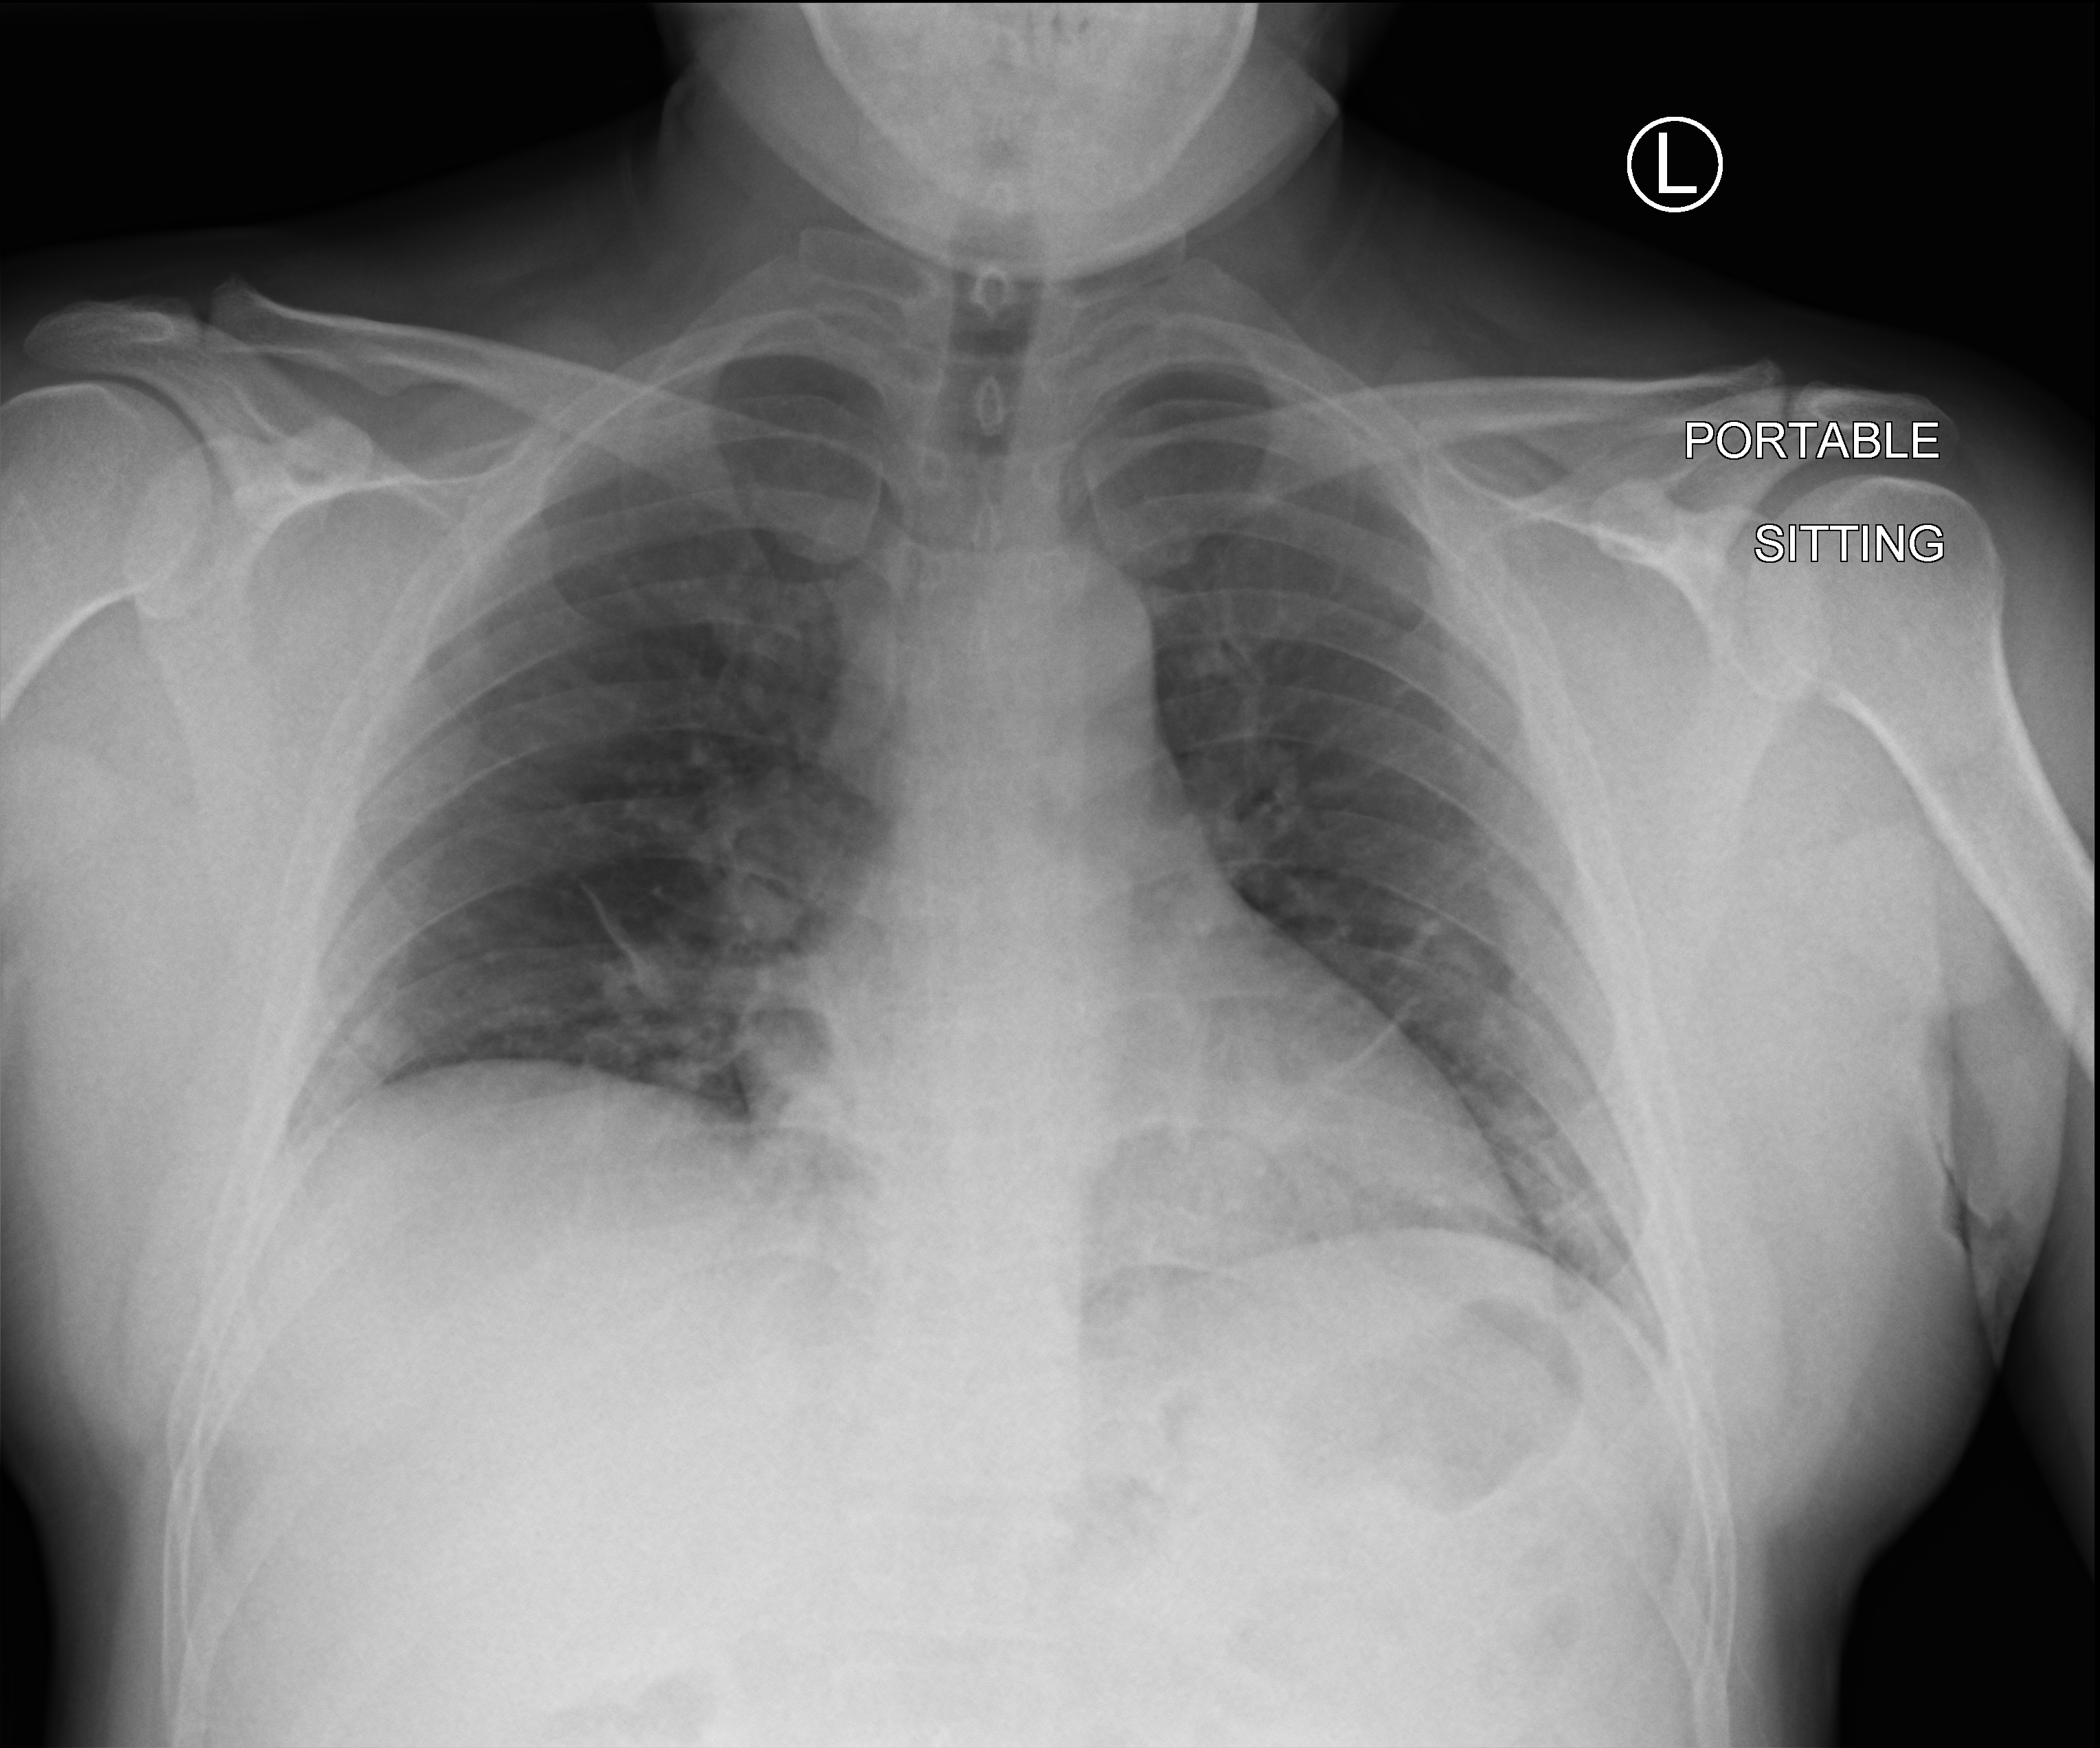
Portable chest radiograph, anteroposterior (AP) projection. Male patient hospitalised with COVID-19, age 18–59 years.
Hospital-stay facts (about this admission, not read from this image; timing relative to this image not recorded):
- length of hospital stay: 1 day